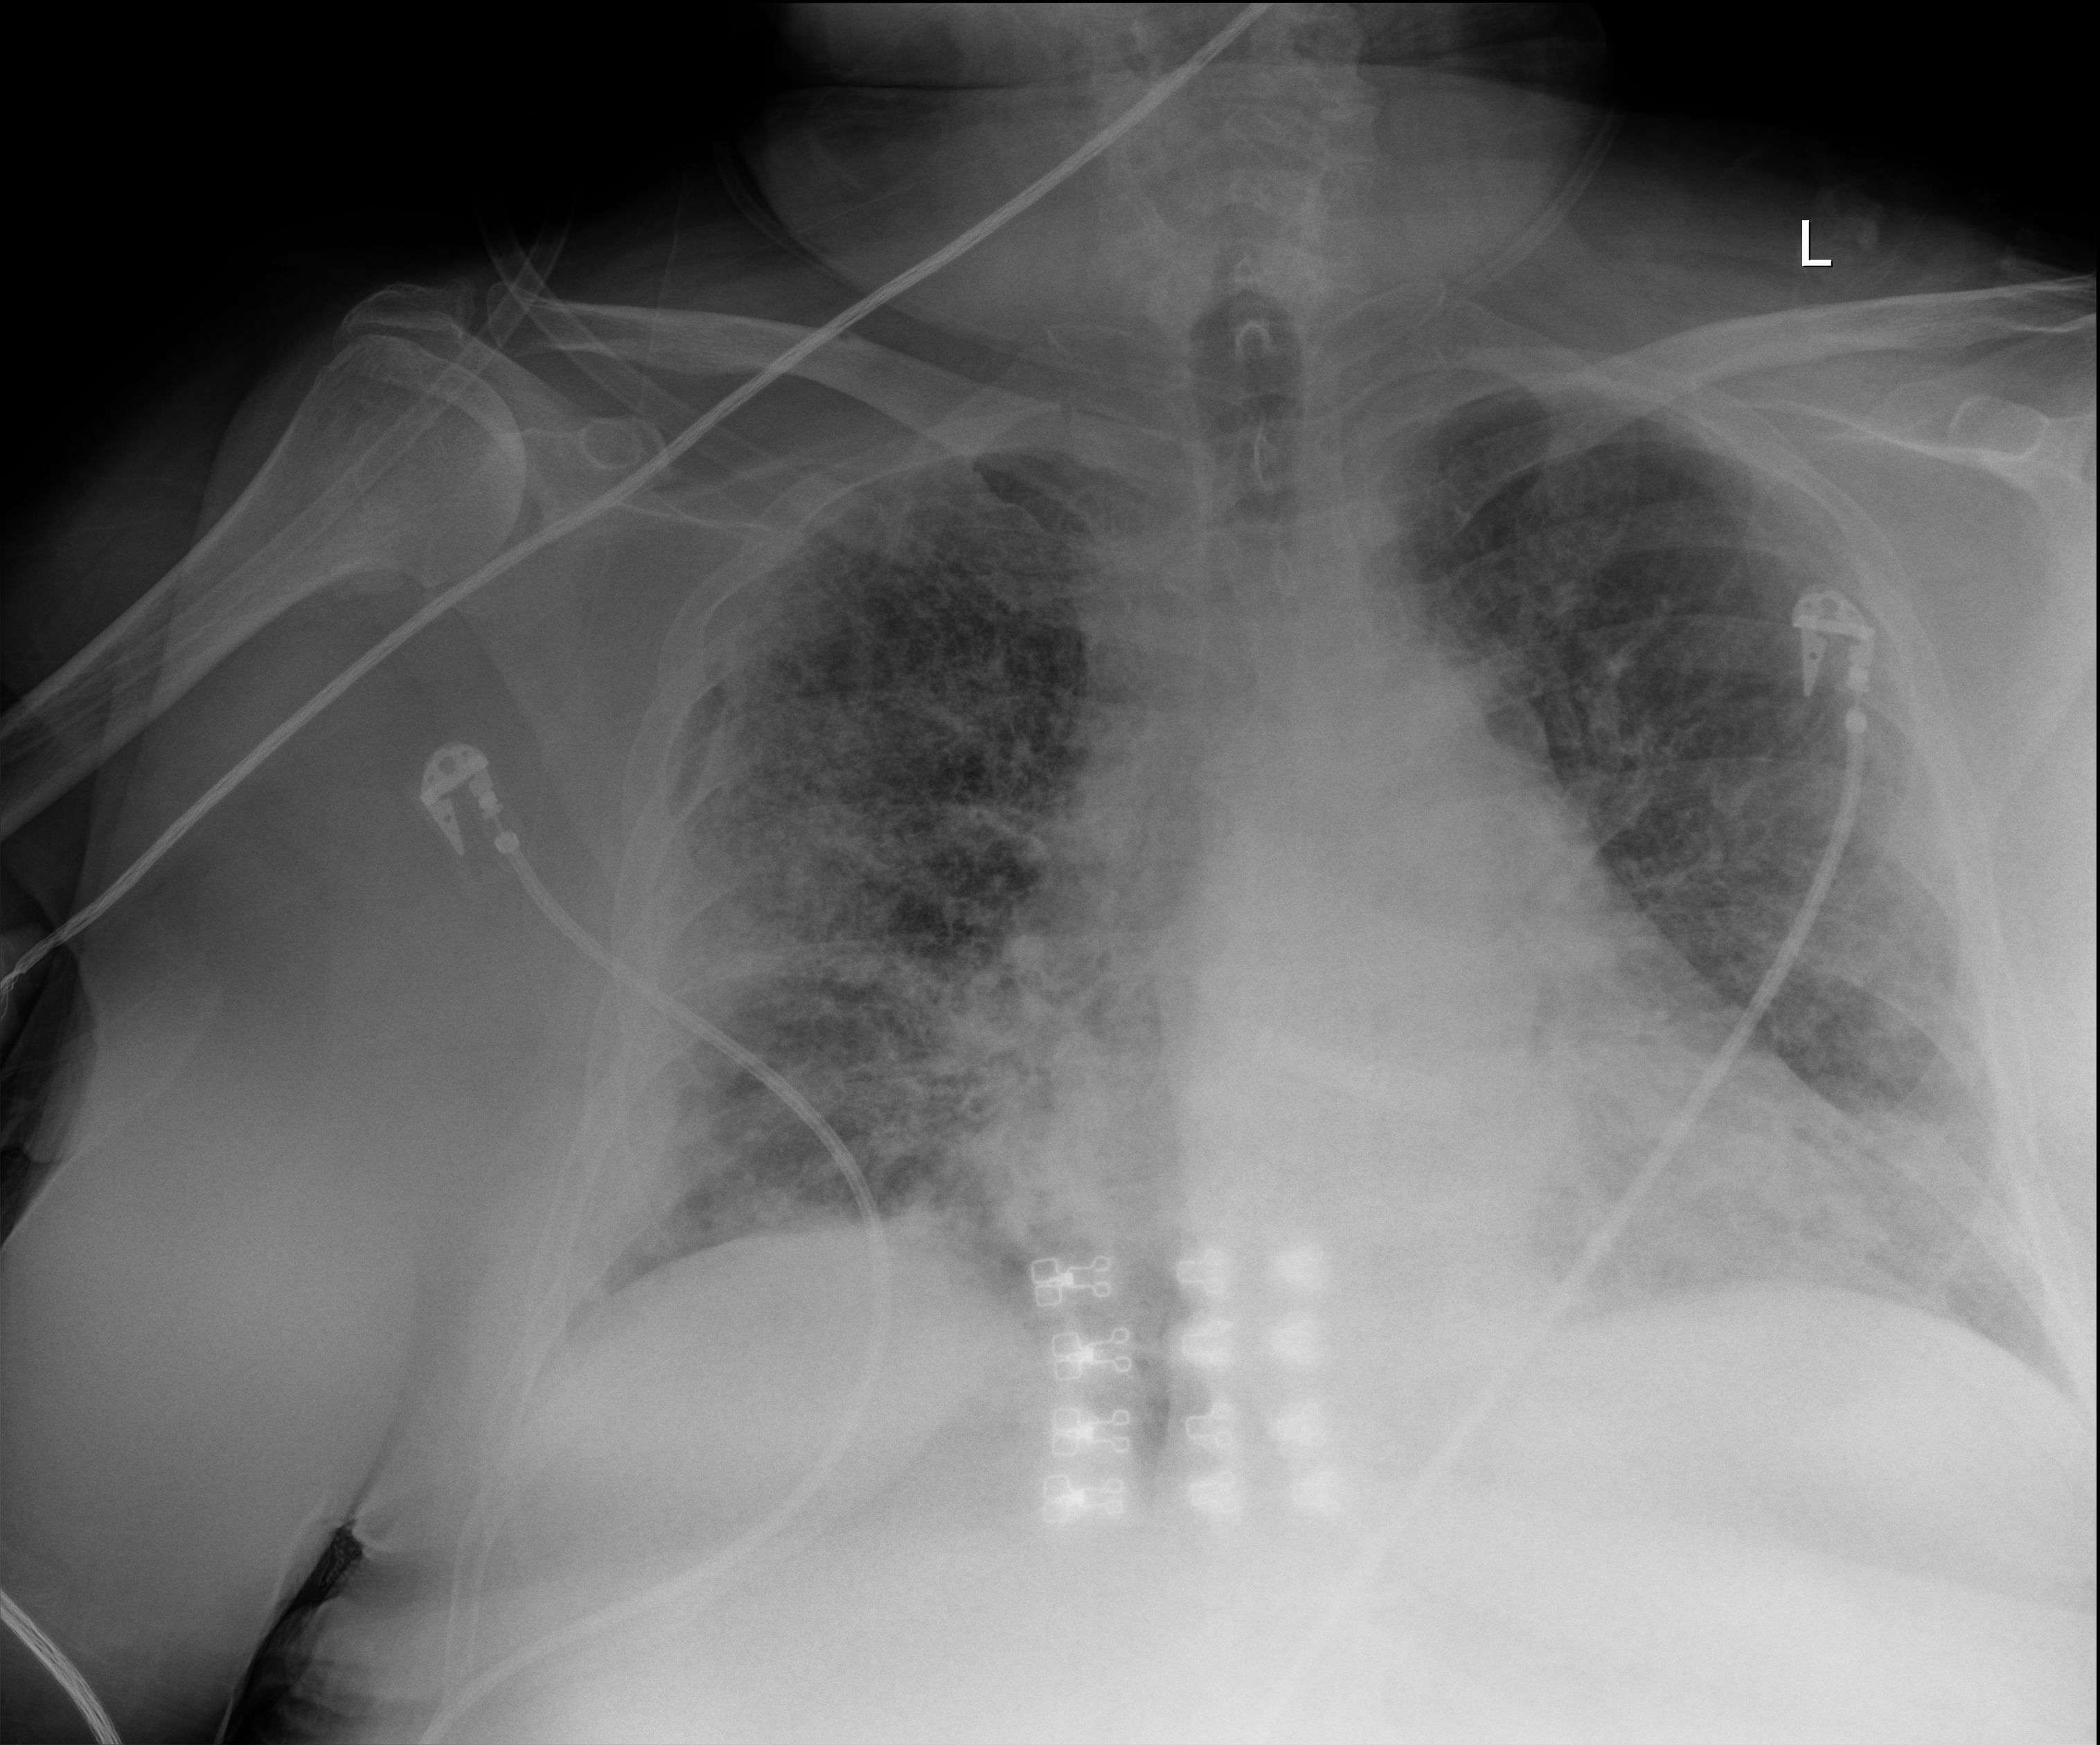
Bedside chest radiograph (digital radiography). Female patient hospitalised with COVID-19, age 60–74 years.
From the hospital-stay record, not from the radiograph (when in the stay this image was taken is not recorded): admitted to intensive care during this hospital stay: yes.